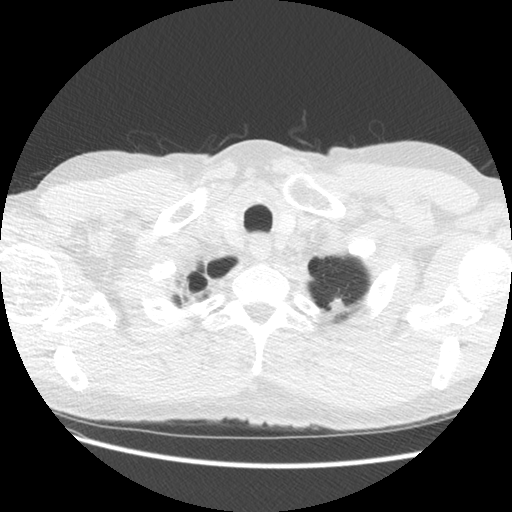
Low-dose screening chest CT, axial slice. Second annual screen. Lung window (W 1500 / L -600 HU). 2.5 mm slice thickness. 512 × 512 image matrix. Male, age 63 years at enrolment. Former smoker at enrolment.
Expert reader's lesion annotation, box from (x=319, y=280) to (x=360, y=317) px. The screening reader recorded 2 non-calcified nodules or masses ≥4 mm on this exam; which of them this box marks is not recorded. Official screen result: positive, other. Lung cancer was diagnosed 104 days after this screen: adenocarcinoma, NOS, left upper lobe, moderately differentiated (G2), stage IB (AJCC 6th edition), 14 mm at pathology.